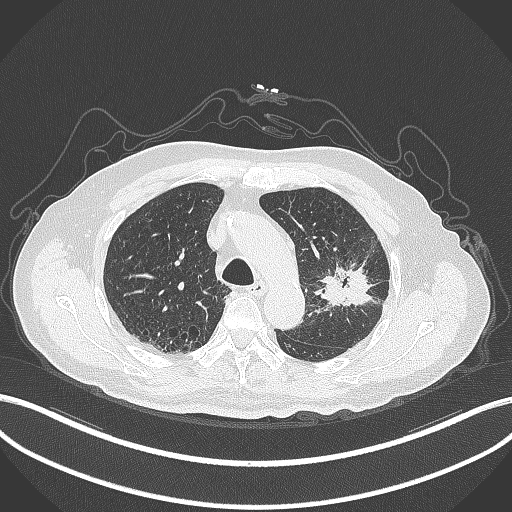
Chest CT, one axial slice. Slice 215 of 331 in the series (ordered by position). Lung window (W 1500 / L -600 HU). 1 mm slice thickness. 512 × 512 image matrix, field of view 400 × 400 mm. Male patient, age 79 years. Case-level facts recorded for this patient, not image findings: clinical TNM (as recorded): T2a N1 M1.
Outlined on this slice (bounding box drawn by a radiologist):
- lung tumour (recorded histology: adenocarcinoma): bounding box (x1, y1, x2, y2) in pixels: (314, 253, 387, 311)